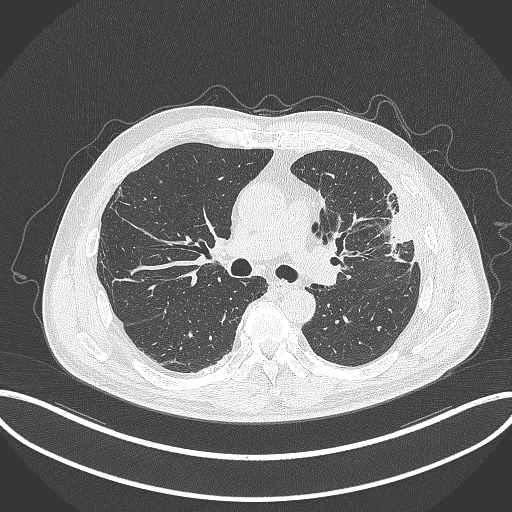
Chest CT, one axial slice. Slice 202 of 382 in the series (ordered by position). 120 kVp. Lung window (W 1500 / L -600 HU). 512 × 512 image matrix, field of view 415 × 415 mm. Patient: male, 64 years. From the clinical record (not read from this slice): clinical TNM (as recorded): T4 N1 M0.
Annotated regions visible in this slice (bounding box drawn by a radiologist):
- lung tumour (recorded histology: adenocarcinoma): box from (x=375, y=182) to (x=414, y=267) px